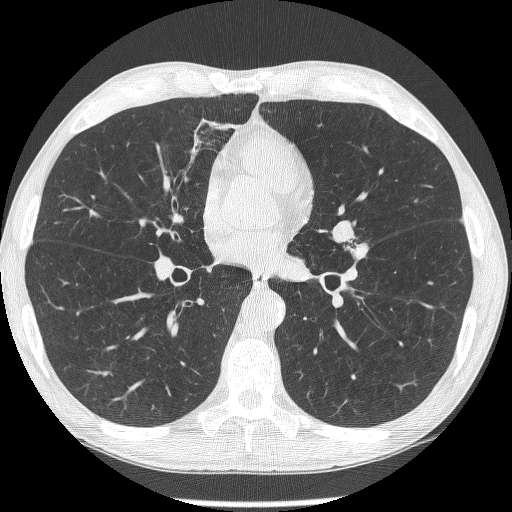
Chest CT (low-dose screening protocol), one axial image. Second annual screen. Lung window (W 1500 / L -600 HU). 1.25 mm slice thickness. Lung (sharp) reconstruction kernel (BONE). Male participant, aged 62 years at enrolment. Former smoker at enrolment.
Expert-annotated lung lesion, bounding box <321,217,370,265> (left, top, right, bottom; pixels). The screening reader recorded 2 non-calcified nodules or masses ≥4 mm on this exam (lingula, lingula); which of them this box marks is not recorded. Later outcome: lung cancer diagnosed 95 days after this screen — small cell carcinoma, NOS, left upper lobe, stage IIIA (AJCC 6th edition).